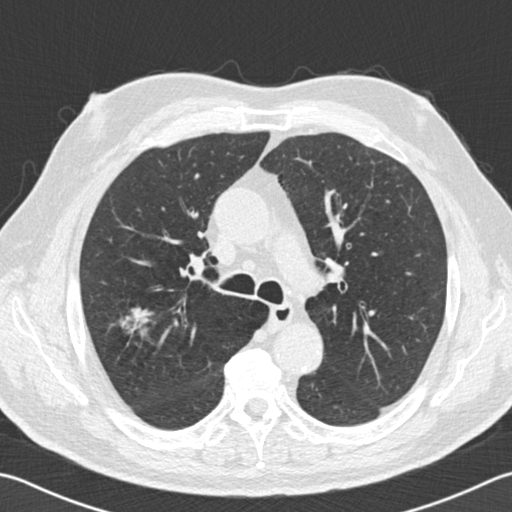
Low-dose screening chest CT, one axial slice. Slice 110 of 162 in the series (ordered by position). Reconstruction kernel B30f. Lung window (W 1500 / L -600 HU). 512 × 512 image matrix, field of view 346 × 346 mm.
Annotated regions visible in this slice (expert manual segmentation):
- lesion 1 (tumor, upper lobe of right lung): bounding box [x1, y1, x2, y2] px = [122, 308, 152, 340]